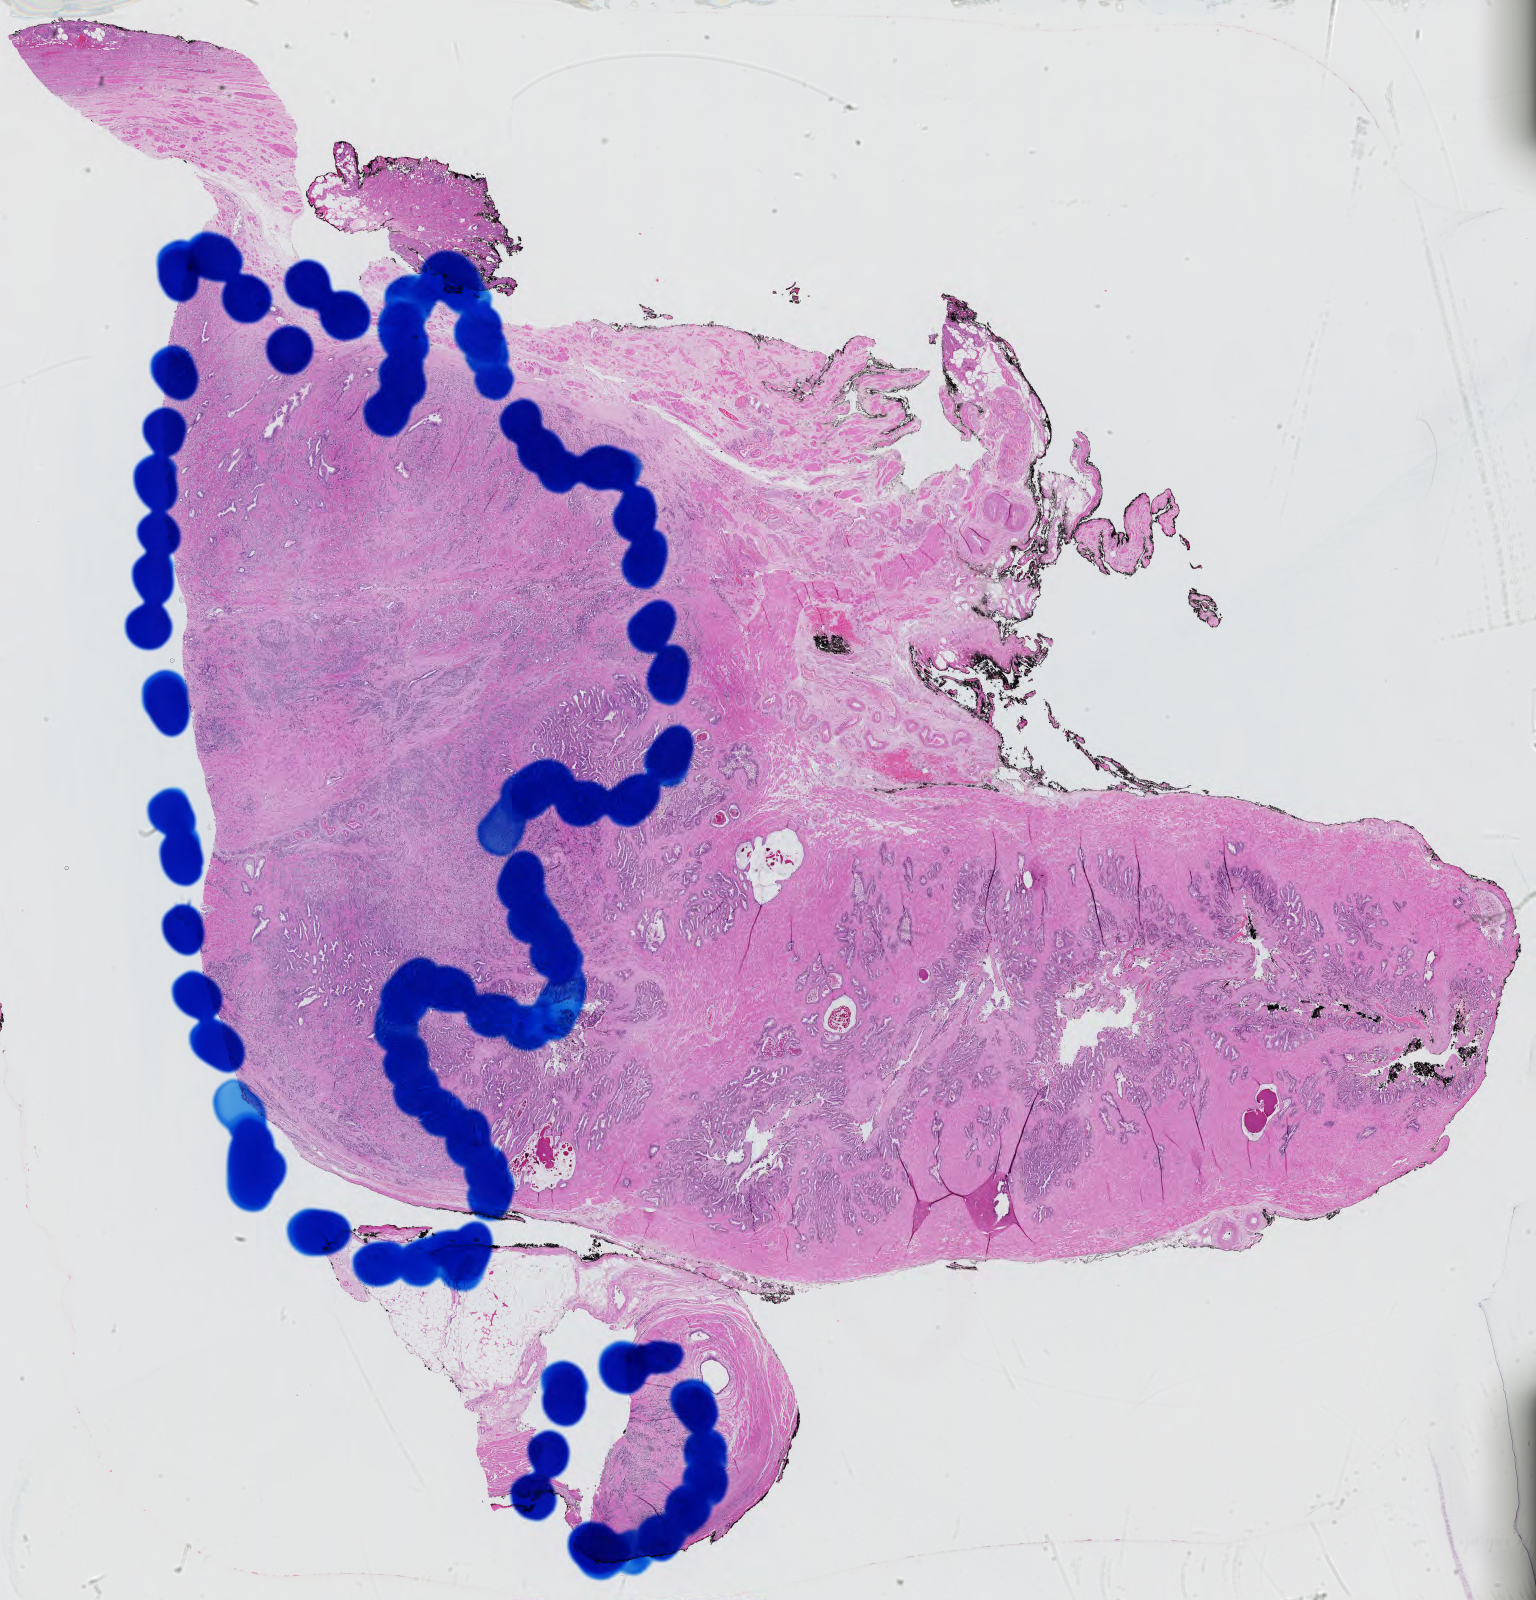
Whole-slide histology image, H&E-stained, shown as a low-resolution overview of the whole scanned area (about 22.3 x 23.2 mm, slide scanned at 40x); FFPE section; prostate, primary tumour sample. Patient: male, age at initial diagnosis 60 years. Gleason score: 9 (4+5).
• laterality: bilateral
• diagnosis: Adenocarcinoma, NOS (prostate gland)